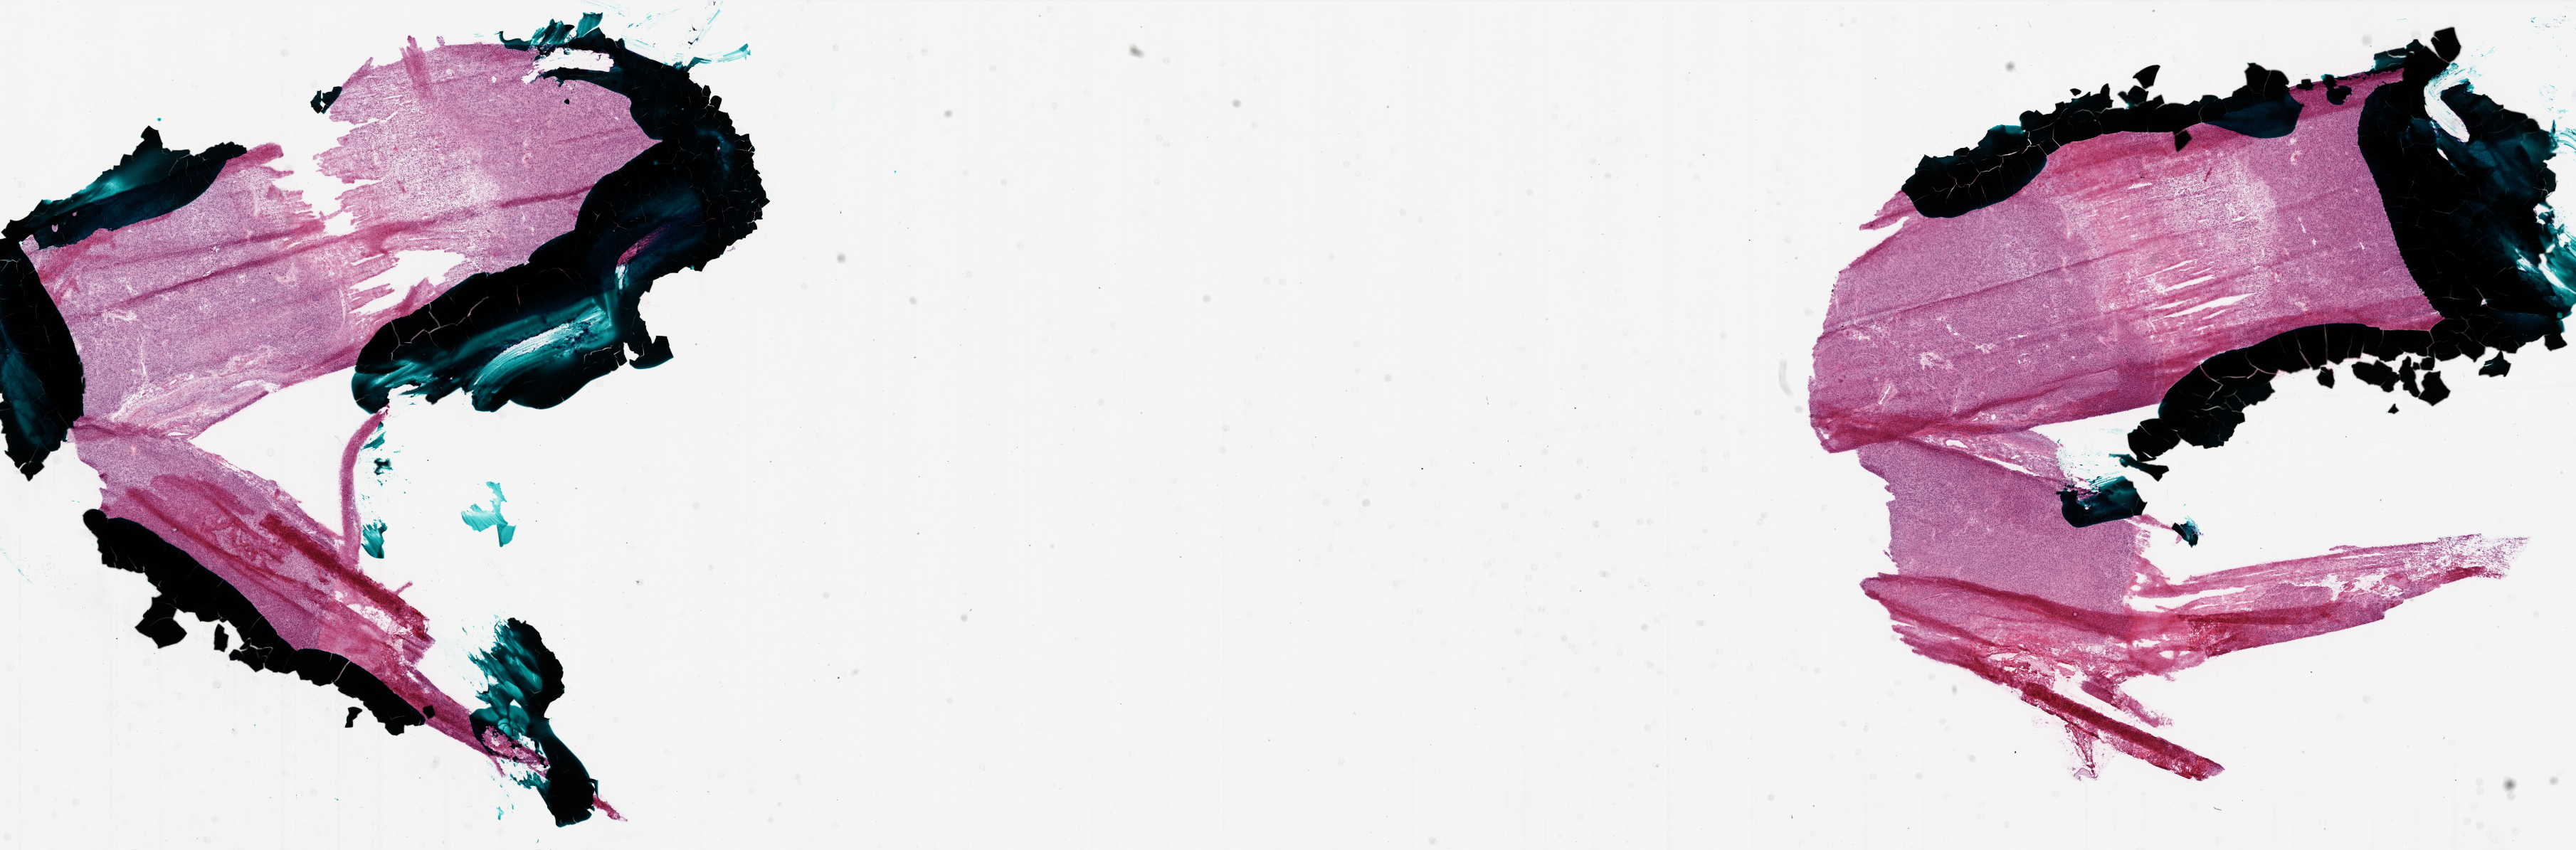
Whole-slide histology image, Hematoxylin and eosin (H&E) stained — whole scanned area (about 29.0 x 9.6 mm) shown as a low-resolution overview, frozen section, sample: primary tumour, brain. Male patient; age at initial diagnosis 76 years. Composition of this section per pathologist review: tumour cells 75%, tumour nuclei 100%, normal cells 0%, stromal cells 0%, necrosis 25%. Infiltration values recorded for this section: lymphocyte infiltration 0%, monocyte infiltration 0%, neutrophil infiltration 0%.
Diagnosis: Glioblastoma.